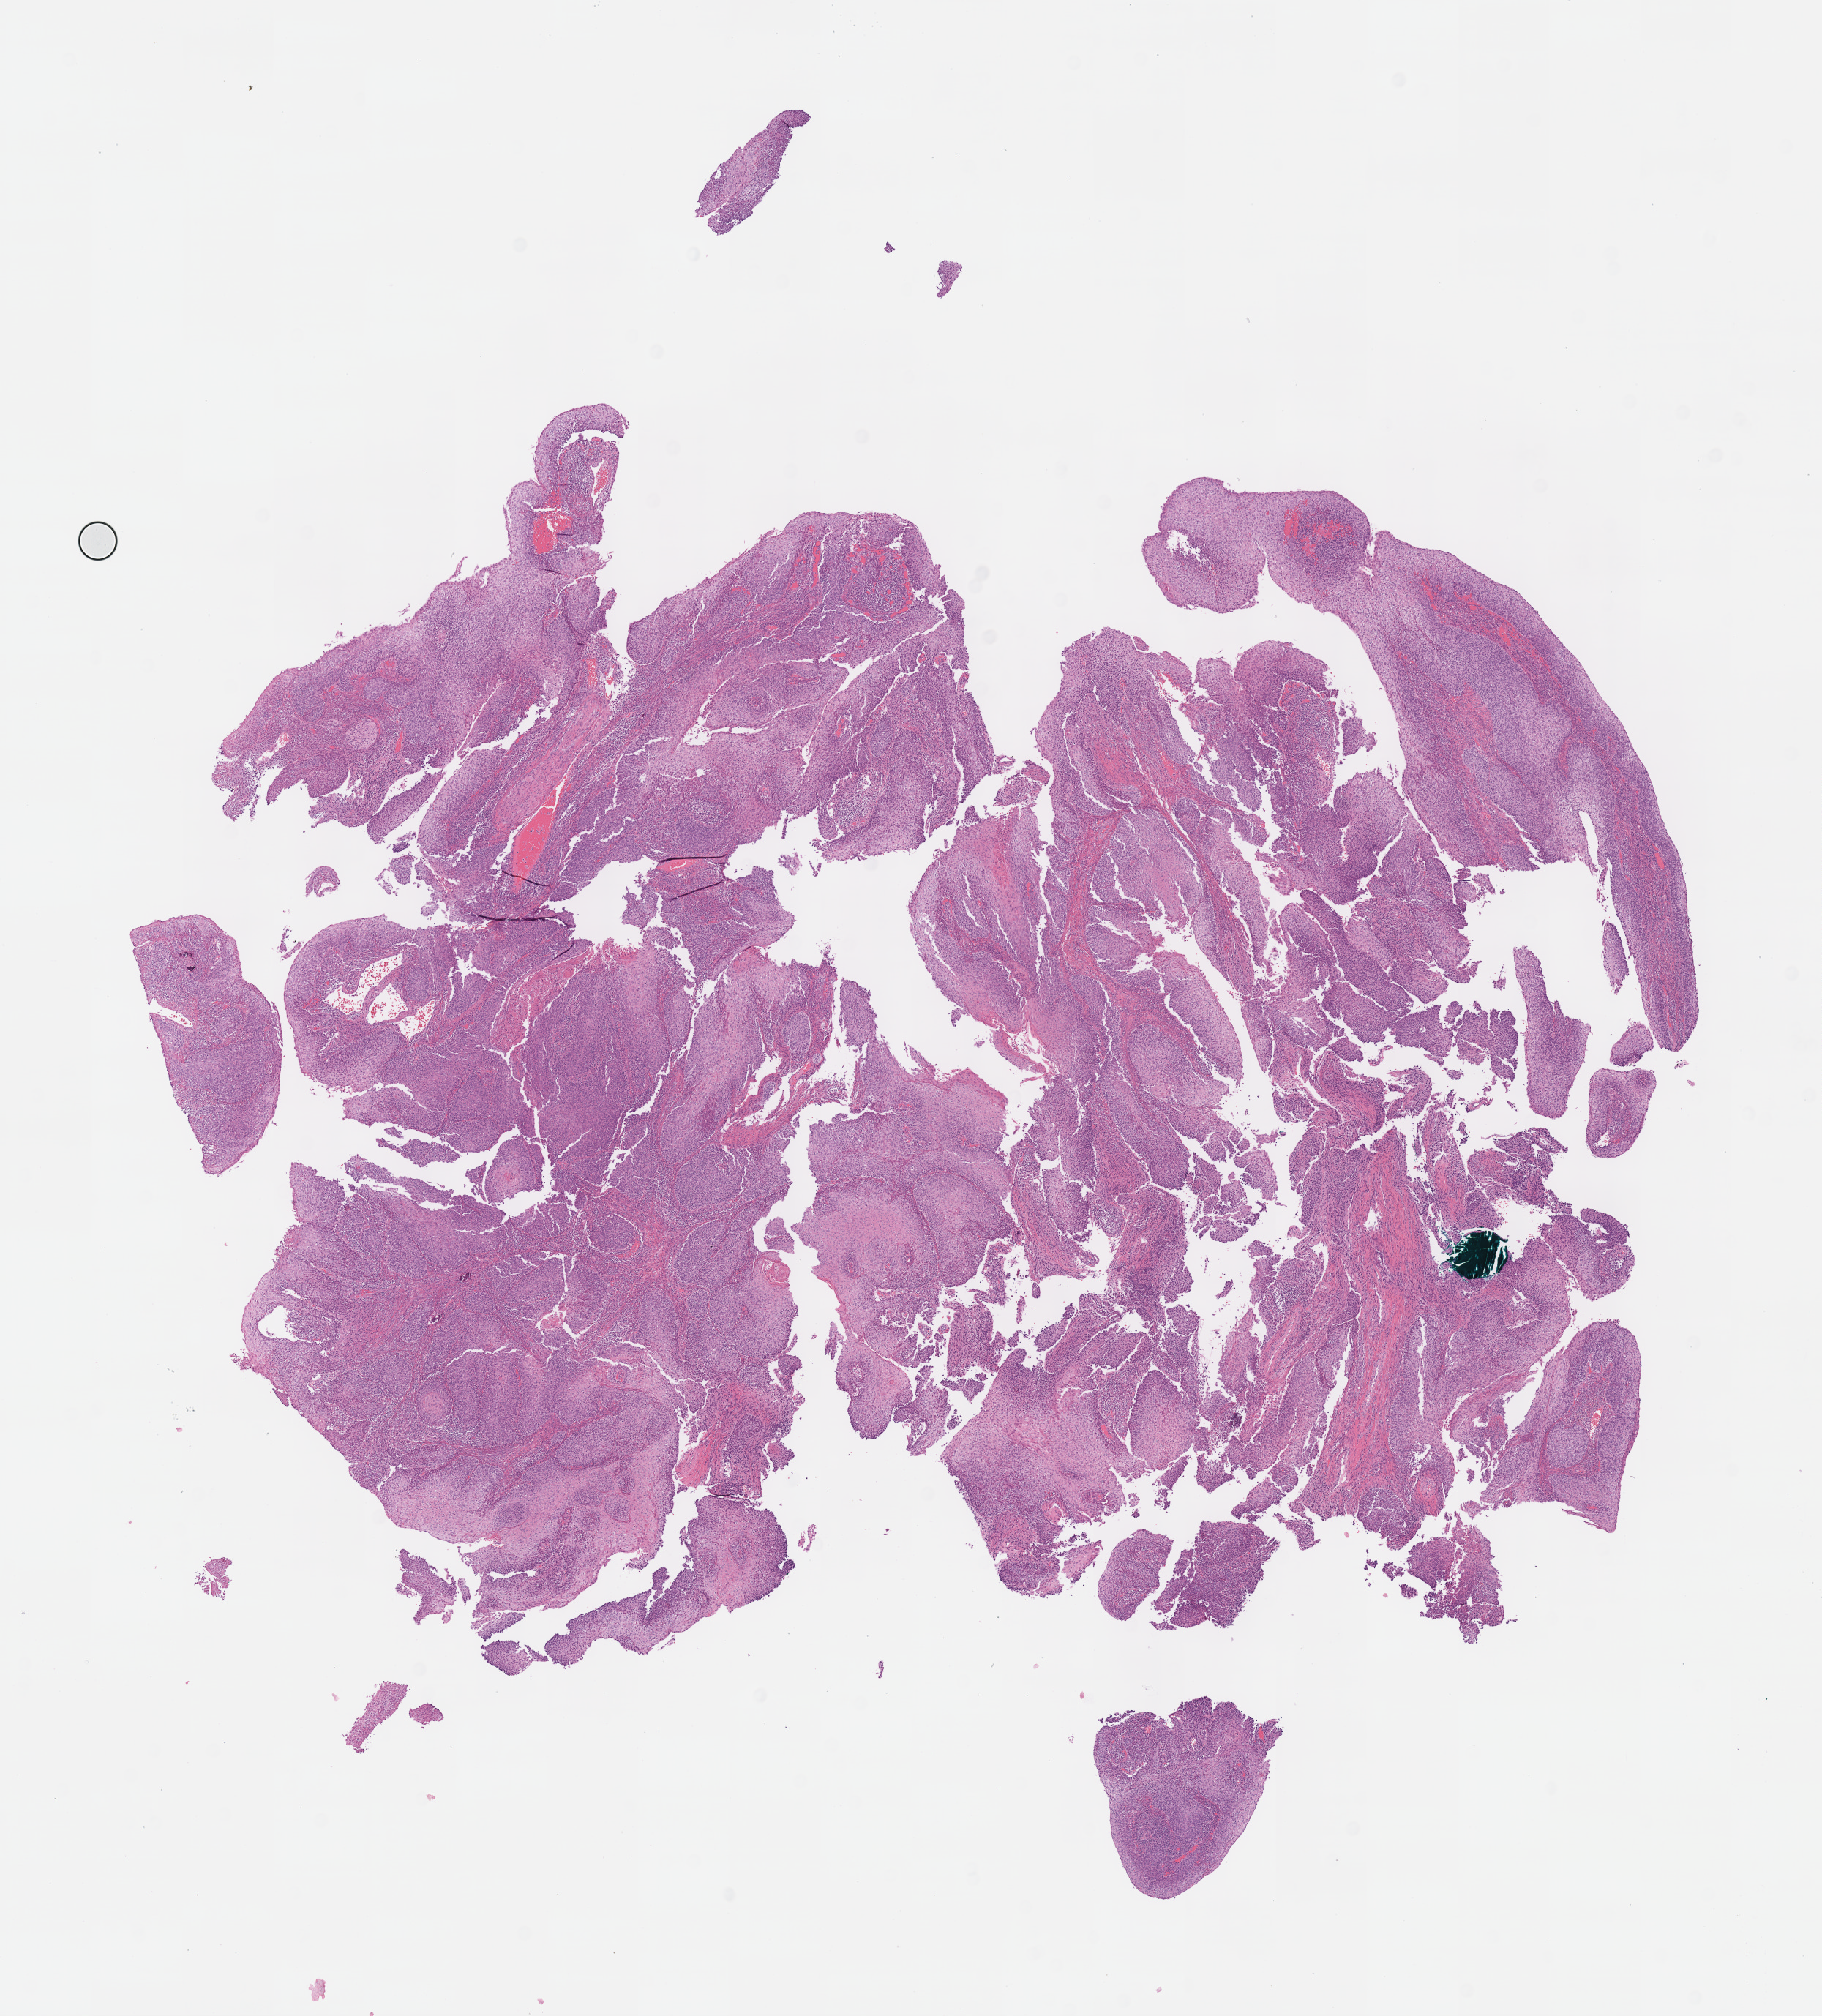
Hematoxylin and eosin (H&E) stained whole-slide image — a low-resolution overview of the entire scanned area, about 9.8 x 10.8 mm, formalin-fixed paraffin-embedded (FFPE) diagnostic section, sample: primary tumour, cervix. Female patient; age at initial diagnosis 43 years. Histologic grade: G2 (moderately differentiated).
- FIGO stage: IIA2
- diagnosis: Squamous cell carcinoma, NOS (cervix uteri)
- lymph nodes positive (case pathology): 0 of 43 examined